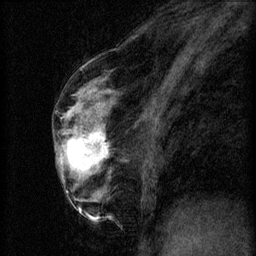
Breast MRI (dynamic contrast-enhanced), one sagittal slice; slice 29 of 60 in the series (ordered by position); 3 images stored at this slice position (order not interpretable as contrast timing); 1.5 T; TE 4.2 ms, TR 8.2 ms; 256 × 256 image matrix, field of view 180 × 180 mm. Female patient, age 56 years.
Annotated regions visible in this slice (semi-automatically segmented with operator editing):
- analysis volume of interest (the breast-tissue region the enhancement analysis was run in; not a lesion): bounding box (x1, y1, x2, y2) in pixels: (60, 124, 111, 179)
- tumour enhancement mask (voxels above the 70 % enhancement threshold inside the analysis volume of interest): (67, 128, 108, 171)